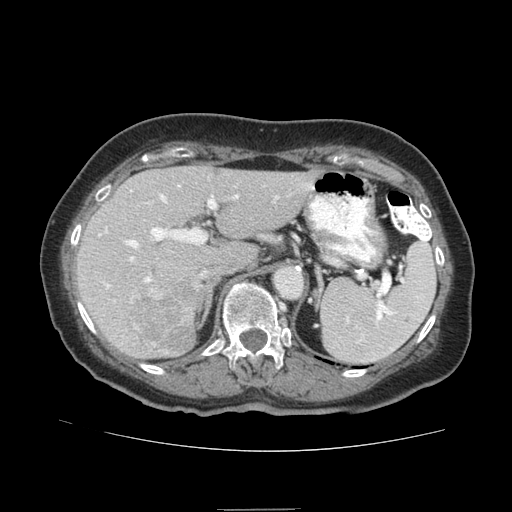
Contrast-enhanced abdominal CT (liver protocol), one axial slice. Position 50 of 95 along the scan axis. Reconstruction kernel STANDARD. Soft-tissue window (W 400 / L 40 HU). 2.5 mm slice thickness. 512 × 512 image matrix, field of view 360 × 360 mm. From the clinical record (not read from this slice): diagnosis: hepatocellular carcinoma (patient treated with transarterial chemoembolisation; whether this scan precedes or follows treatment is not stated here); TNM stage (as recorded): Stage-IVA; Child-Pugh class: B; tumour nodularity: uninodular.
Structures marked on this image (semi-automatic segmentation, software-assisted and operator-edited):
- liver parenchyma outside the tumour (the mass and vessels are separate outlines, so this box may not span the whole liver): bounding box [x1, y1, x2, y2] px = [76, 166, 318, 358]
- mass: [132, 275, 202, 354]
- liver vessels: [99, 185, 313, 289]